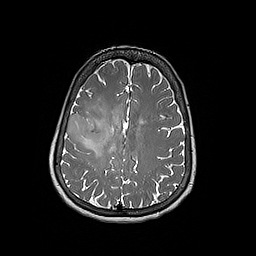
Brain MRI from a brain-tumour surgery series, one axial slice. Position 72 of 192 along the scan axis. 1 mm slice thickness. 256 × 256 image matrix, field of view 250 × 250 mm. From the clinical record (not read from this slice): histopathology: Oligodendroglioma; WHO grade: 3; IDH mutation: yes.
Outlined on this slice (outlined manually by an expert reader):
- tumour: bounding box <66,113,110,151> (left, top, right, bottom; pixels)